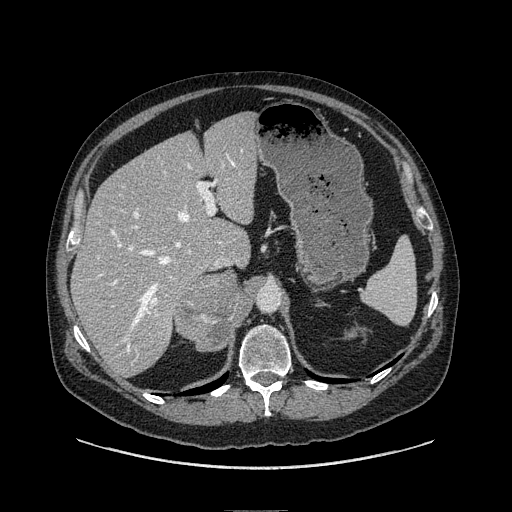
Contrast-enhanced abdominal CT, one axial slice. Position 66 of 149 along the scan axis. Soft-tissue window (W 400 / L 40 HU). 1.25 mm slice thickness. 512 × 512 image matrix, field of view 440 × 440 mm. Male patient. Case-level facts recorded for this patient, not image findings: diagnosis: adrenocortical carcinoma; tumour side: right adrenal; tumour size at pathology: 7.5 cm; Ki-67 index: 15 %.
Structures marked on this image (semi-automatically segmented with operator editing):
- mass: bounding box <177,269,244,351> (left, top, right, bottom; pixels)